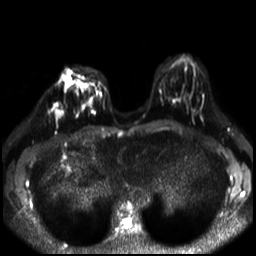
Breast MRI, one axial slice. Slice 10 of 30 in the series (ordered by position). Diffusion-weighted series; image 2 of 4 stored at this slice position (different b-values; order by instance number). 3 T. 4 mm slice thickness. 256 × 256 image matrix. Female patient.
Annotated regions visible in this slice (expert manual segmentation):
- tumour on diffusion-weighted imaging: bounding box (x1, y1, x2, y2) in pixels: (55, 103, 63, 116)